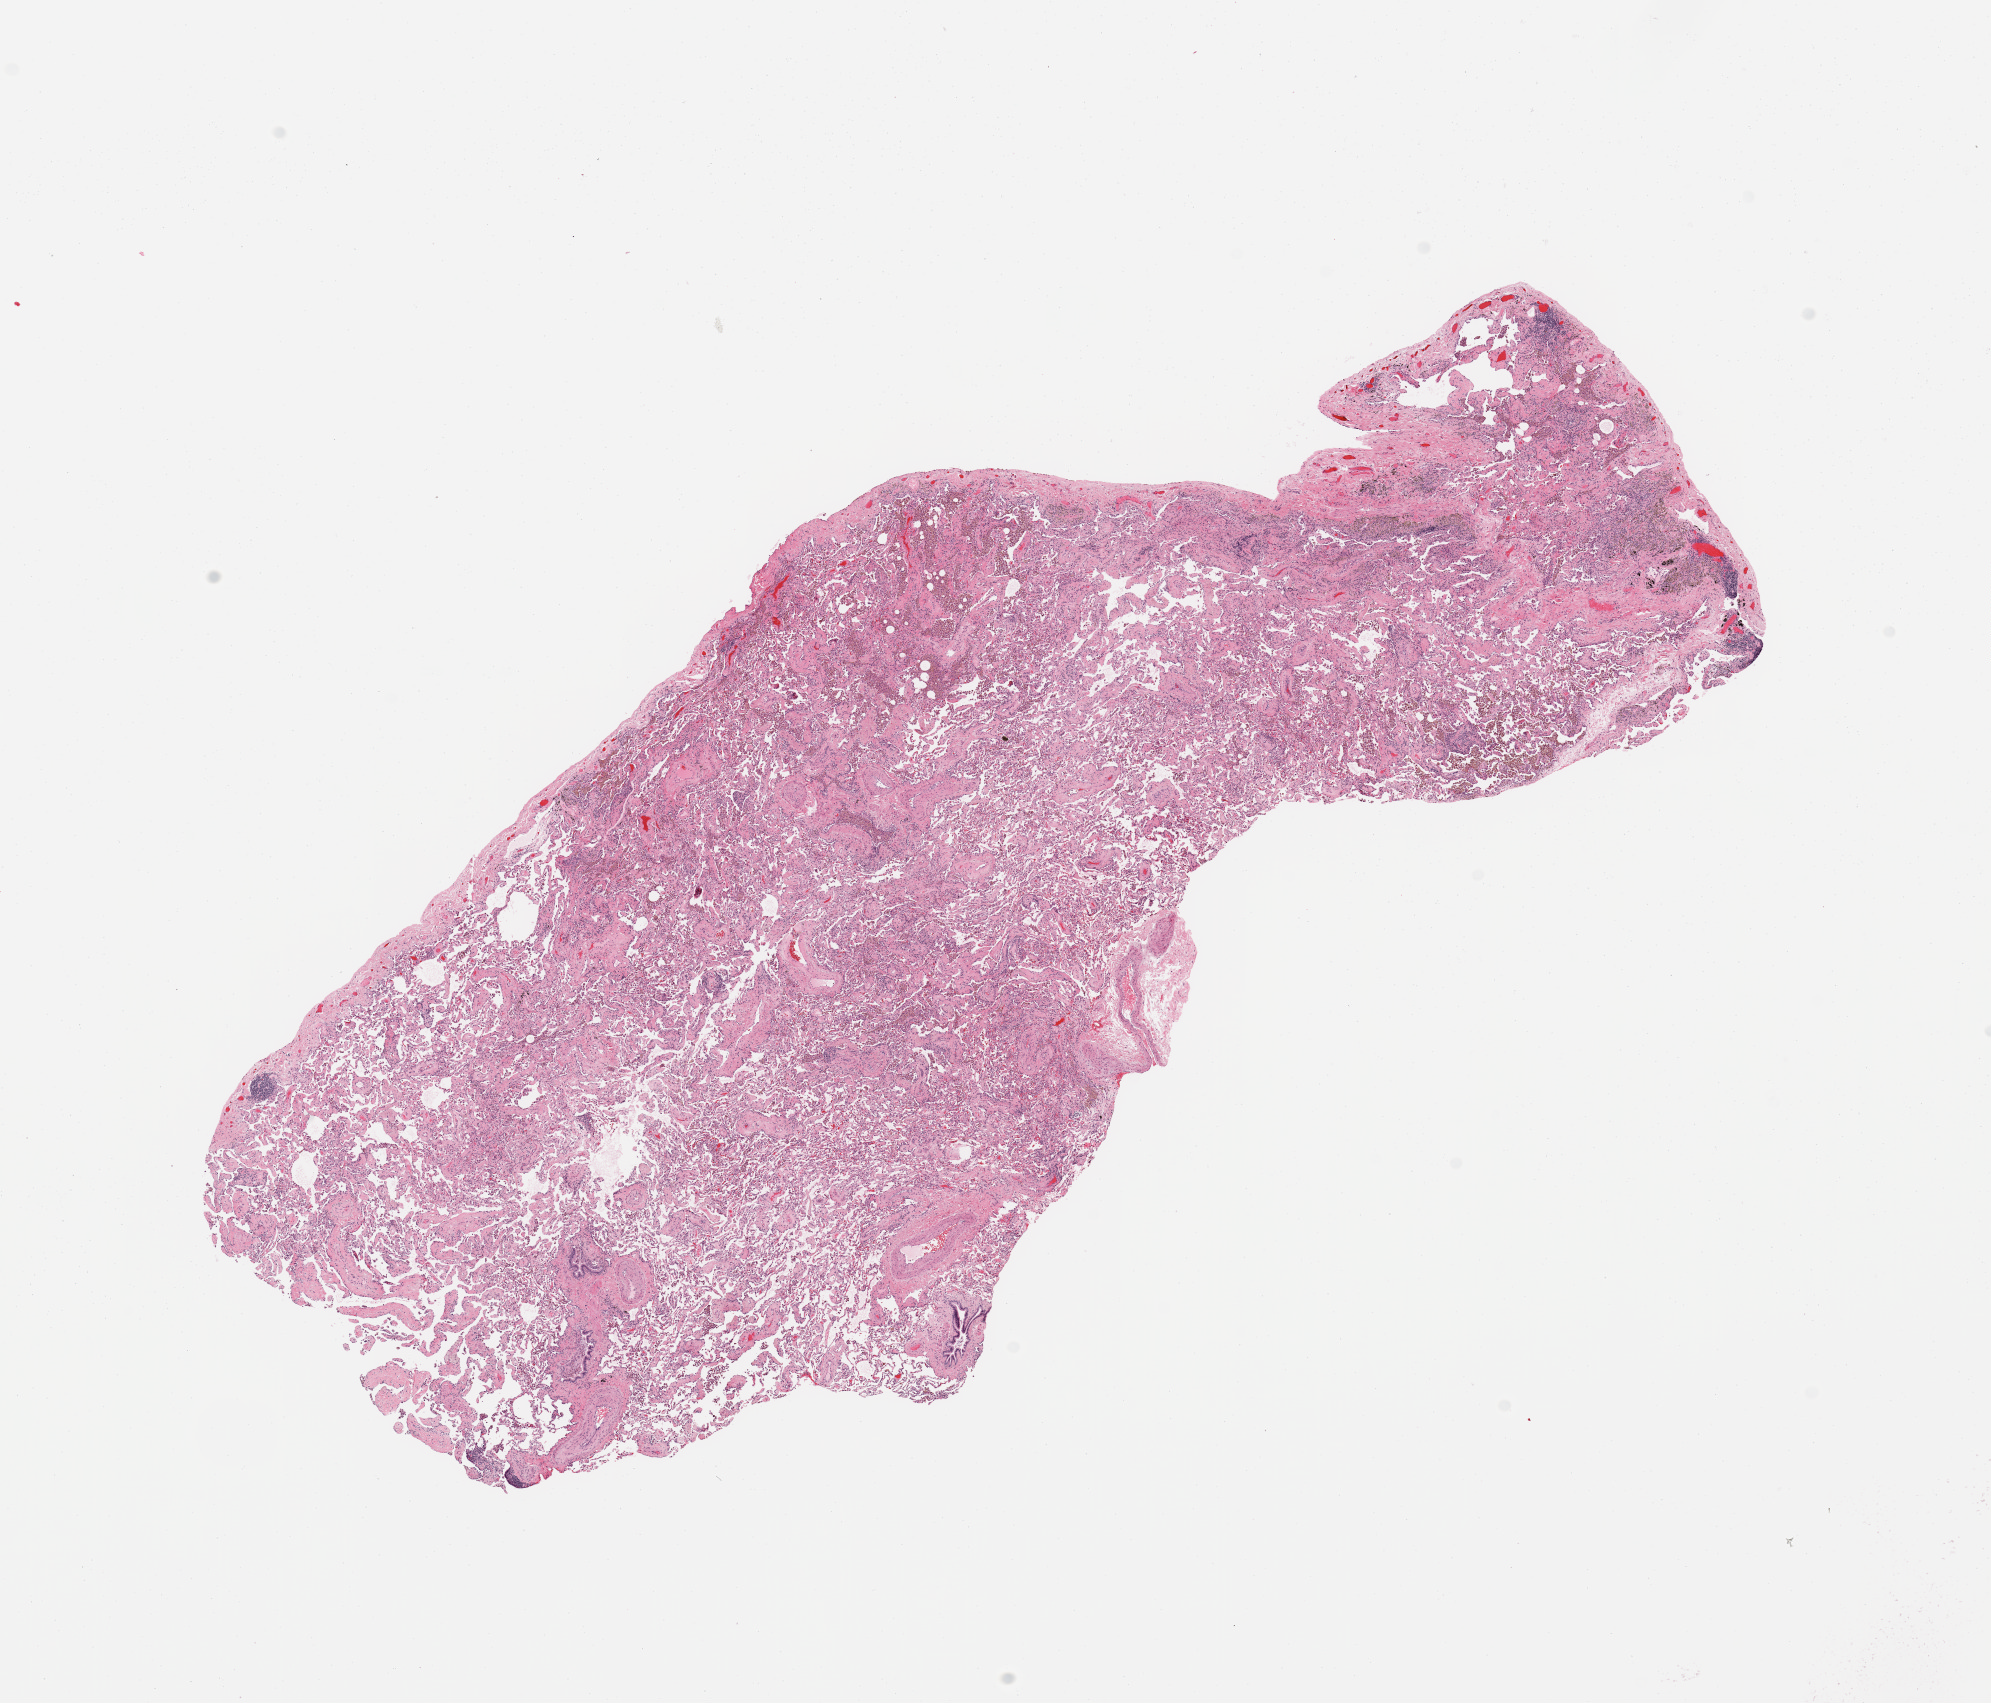
Hematoxylin and eosin (H&E) stained whole-slide image, shown as a low-resolution overview of the whole scanned area (about 15.8 x 13.5 mm); normal (non-tumour) tissue sample, sampled site: lung. 76-year-old male patient.
This section: normal (non-tumour) tissue from the same patient. Patient diagnosis: Adenocarcinoma, NOS.